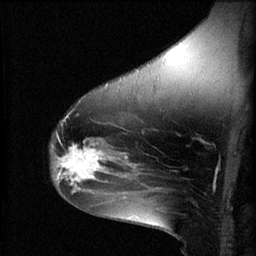
Breast MRI (dynamic contrast-enhanced), one sagittal slice; position 41 of 60 along the scan axis; 3 images stored at this slice position (order not interpretable as contrast timing); 1.5 T; TE 4.2 ms, TR 8.2 ms; 256 × 256 image matrix, field of view 180 × 180 mm. Patient: female, 49 years.
Annotated regions visible in this slice (semi-automatically segmented with operator editing):
- analysis volume of interest (the breast-tissue region the enhancement analysis was run in; not a lesion): bounding box (x1, y1, x2, y2) in pixels: (51, 136, 109, 187)
- tumour enhancement mask (voxels above the 70 % enhancement threshold inside the analysis volume of interest): (56, 136, 109, 187)